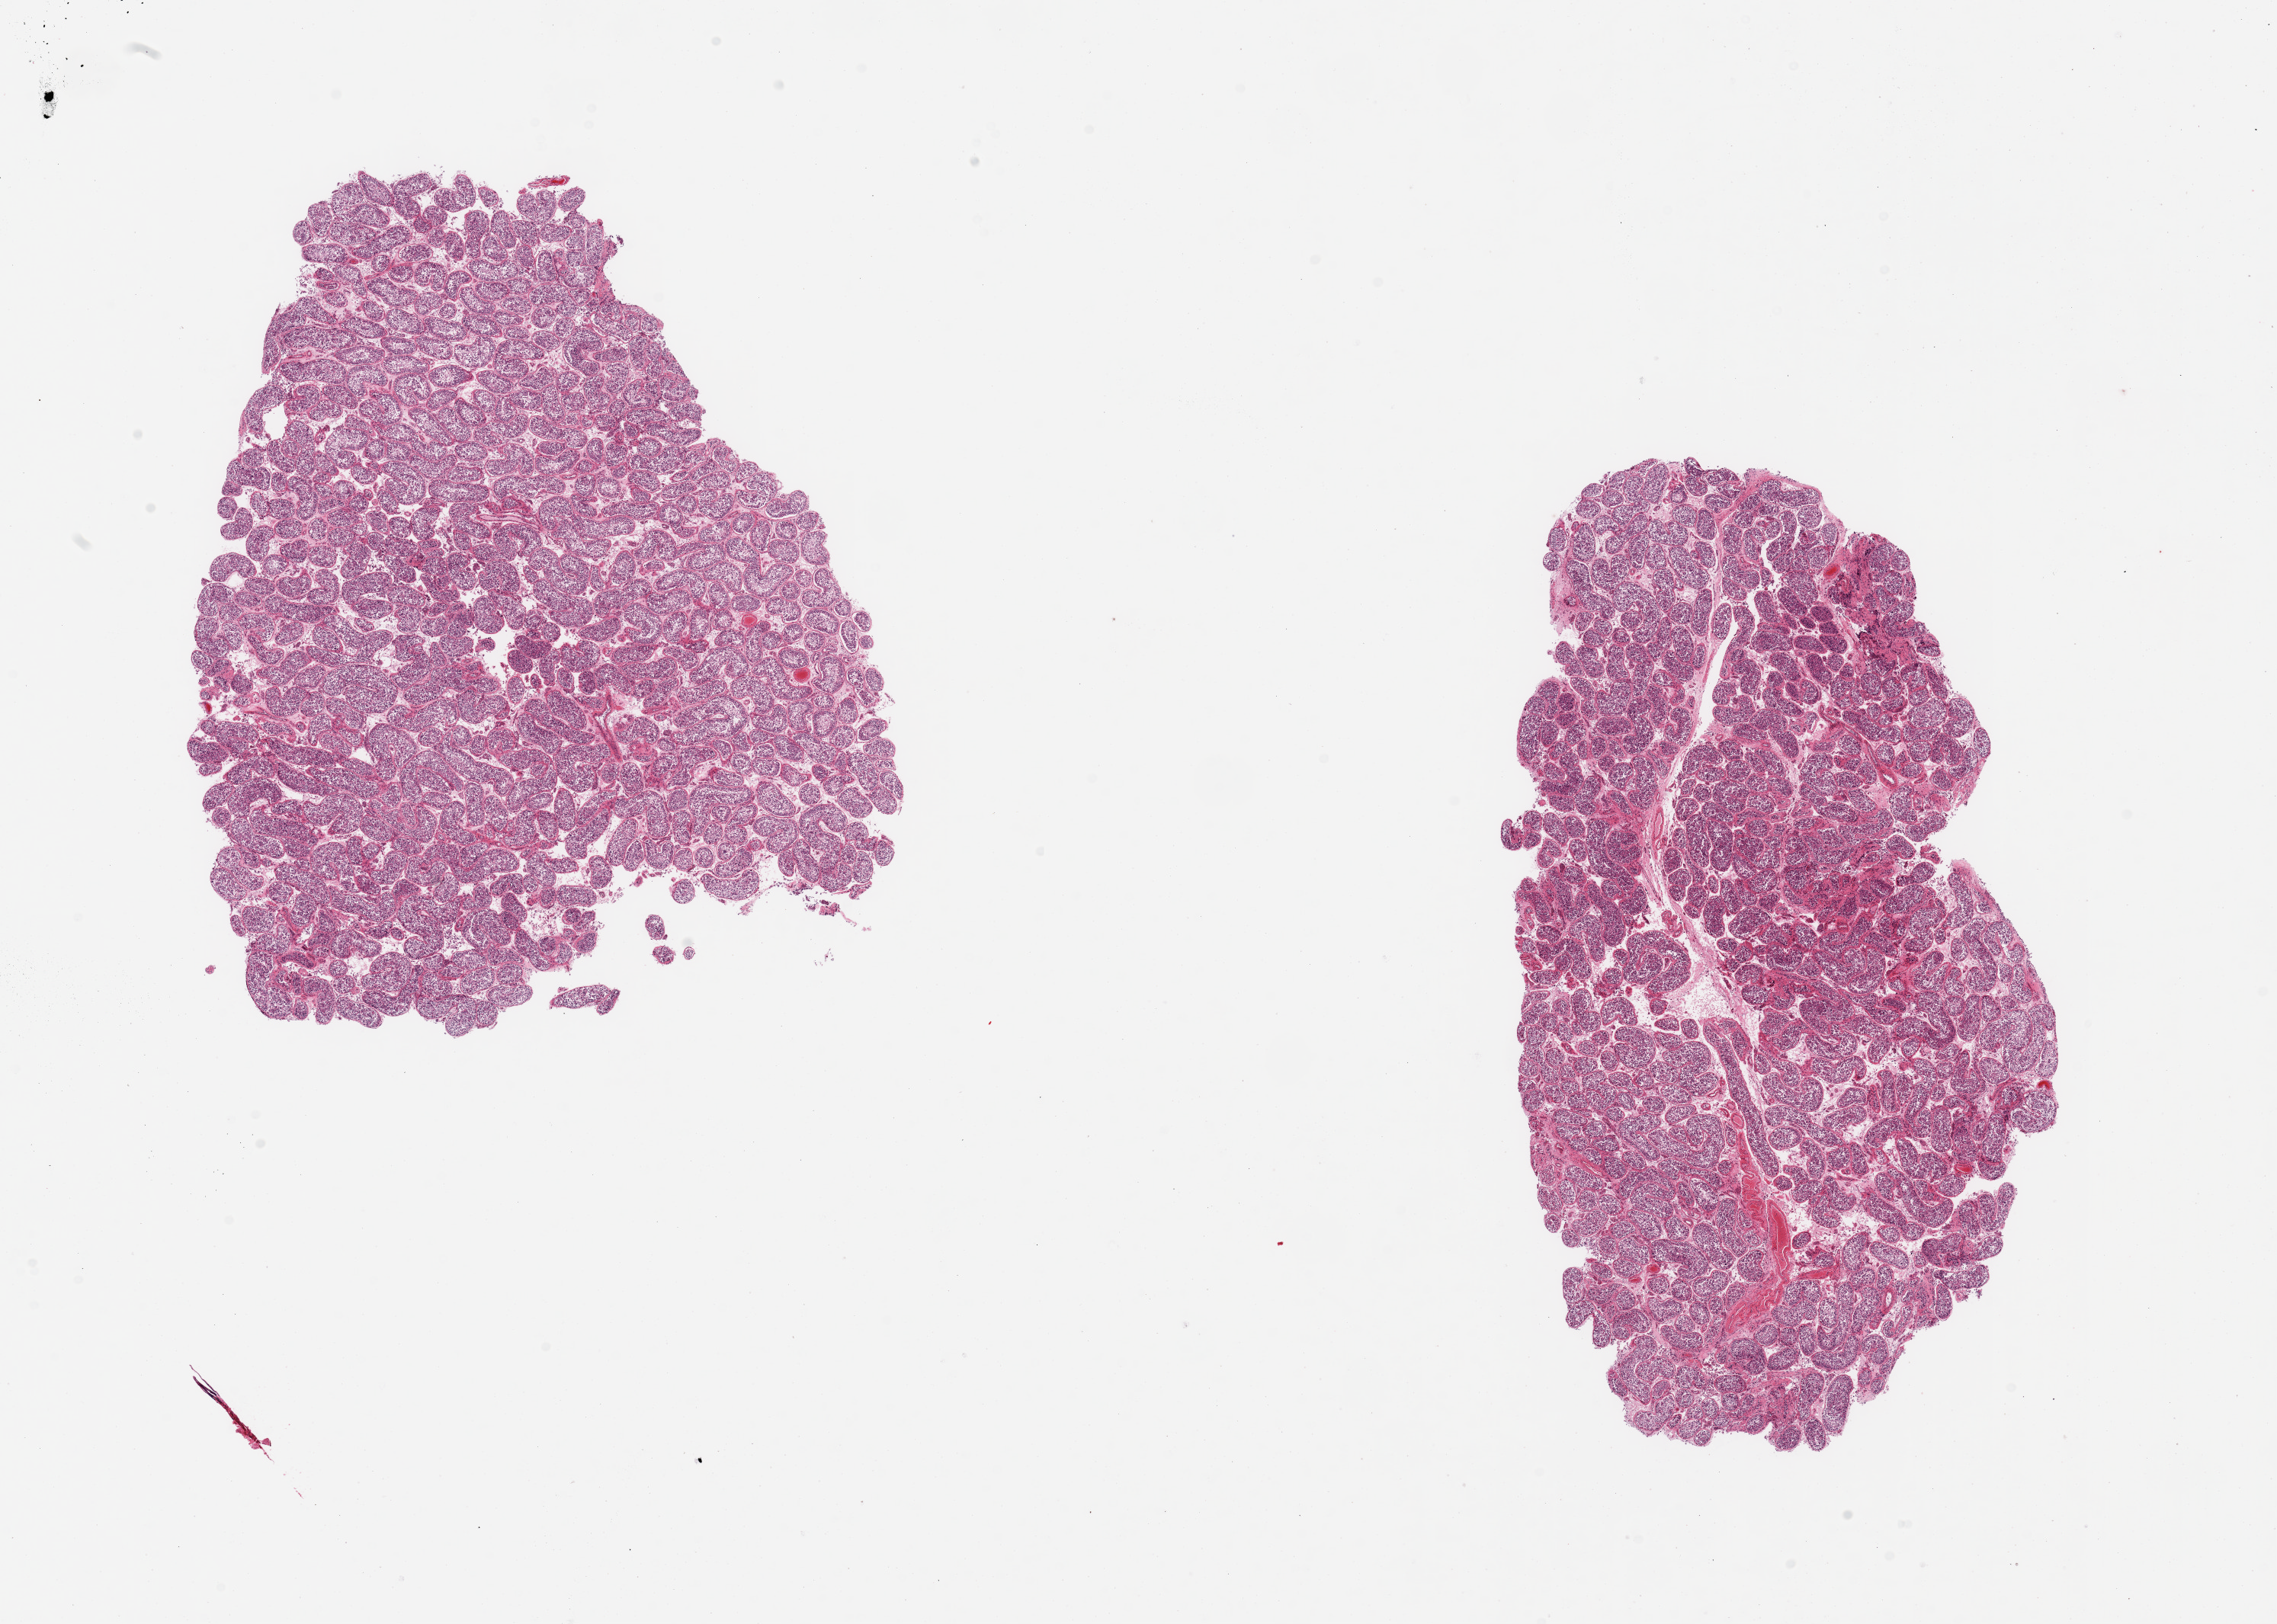
H&E whole-slide image, brightfield — shown as a low-resolution overview of the whole scanned area (about 23.6 x 16.9 mm, slide scanned at 20x). PAXgene-fixed paraffin-embedded (PFPE) section. Section of testis (target tissue). Donor tissue sample. Donor: male.
- pathologist's review note for this sample: 2 pieces; active spermatogenesis